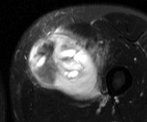
MRI of an extremity soft-tissue mass, one axial slice. Slice 21 of 52 in the series (ordered by position). T2-weighted fat-saturated. MR volume resampled by the dataset authors to the PET/CT grid (not the native acquisition matrix). 3.27 mm slice thickness. 147 × 122 image matrix, field of view 144 × 119 mm. Male patient. Case-level facts recorded for this patient, not image findings: histological type: pleiomorphic liposarcoma; grade: high; site of the primary tumour: left thigh.
Annotated regions visible in this slice (expert contour drawn on MRI and transferred to this co-registered scan by the dataset authors):
- gross tumour volume including surrounding oedema: bounding box <27,21,110,100> (left, top, right, bottom; pixels)
- gross tumour volume (mass): <27,28,101,99>